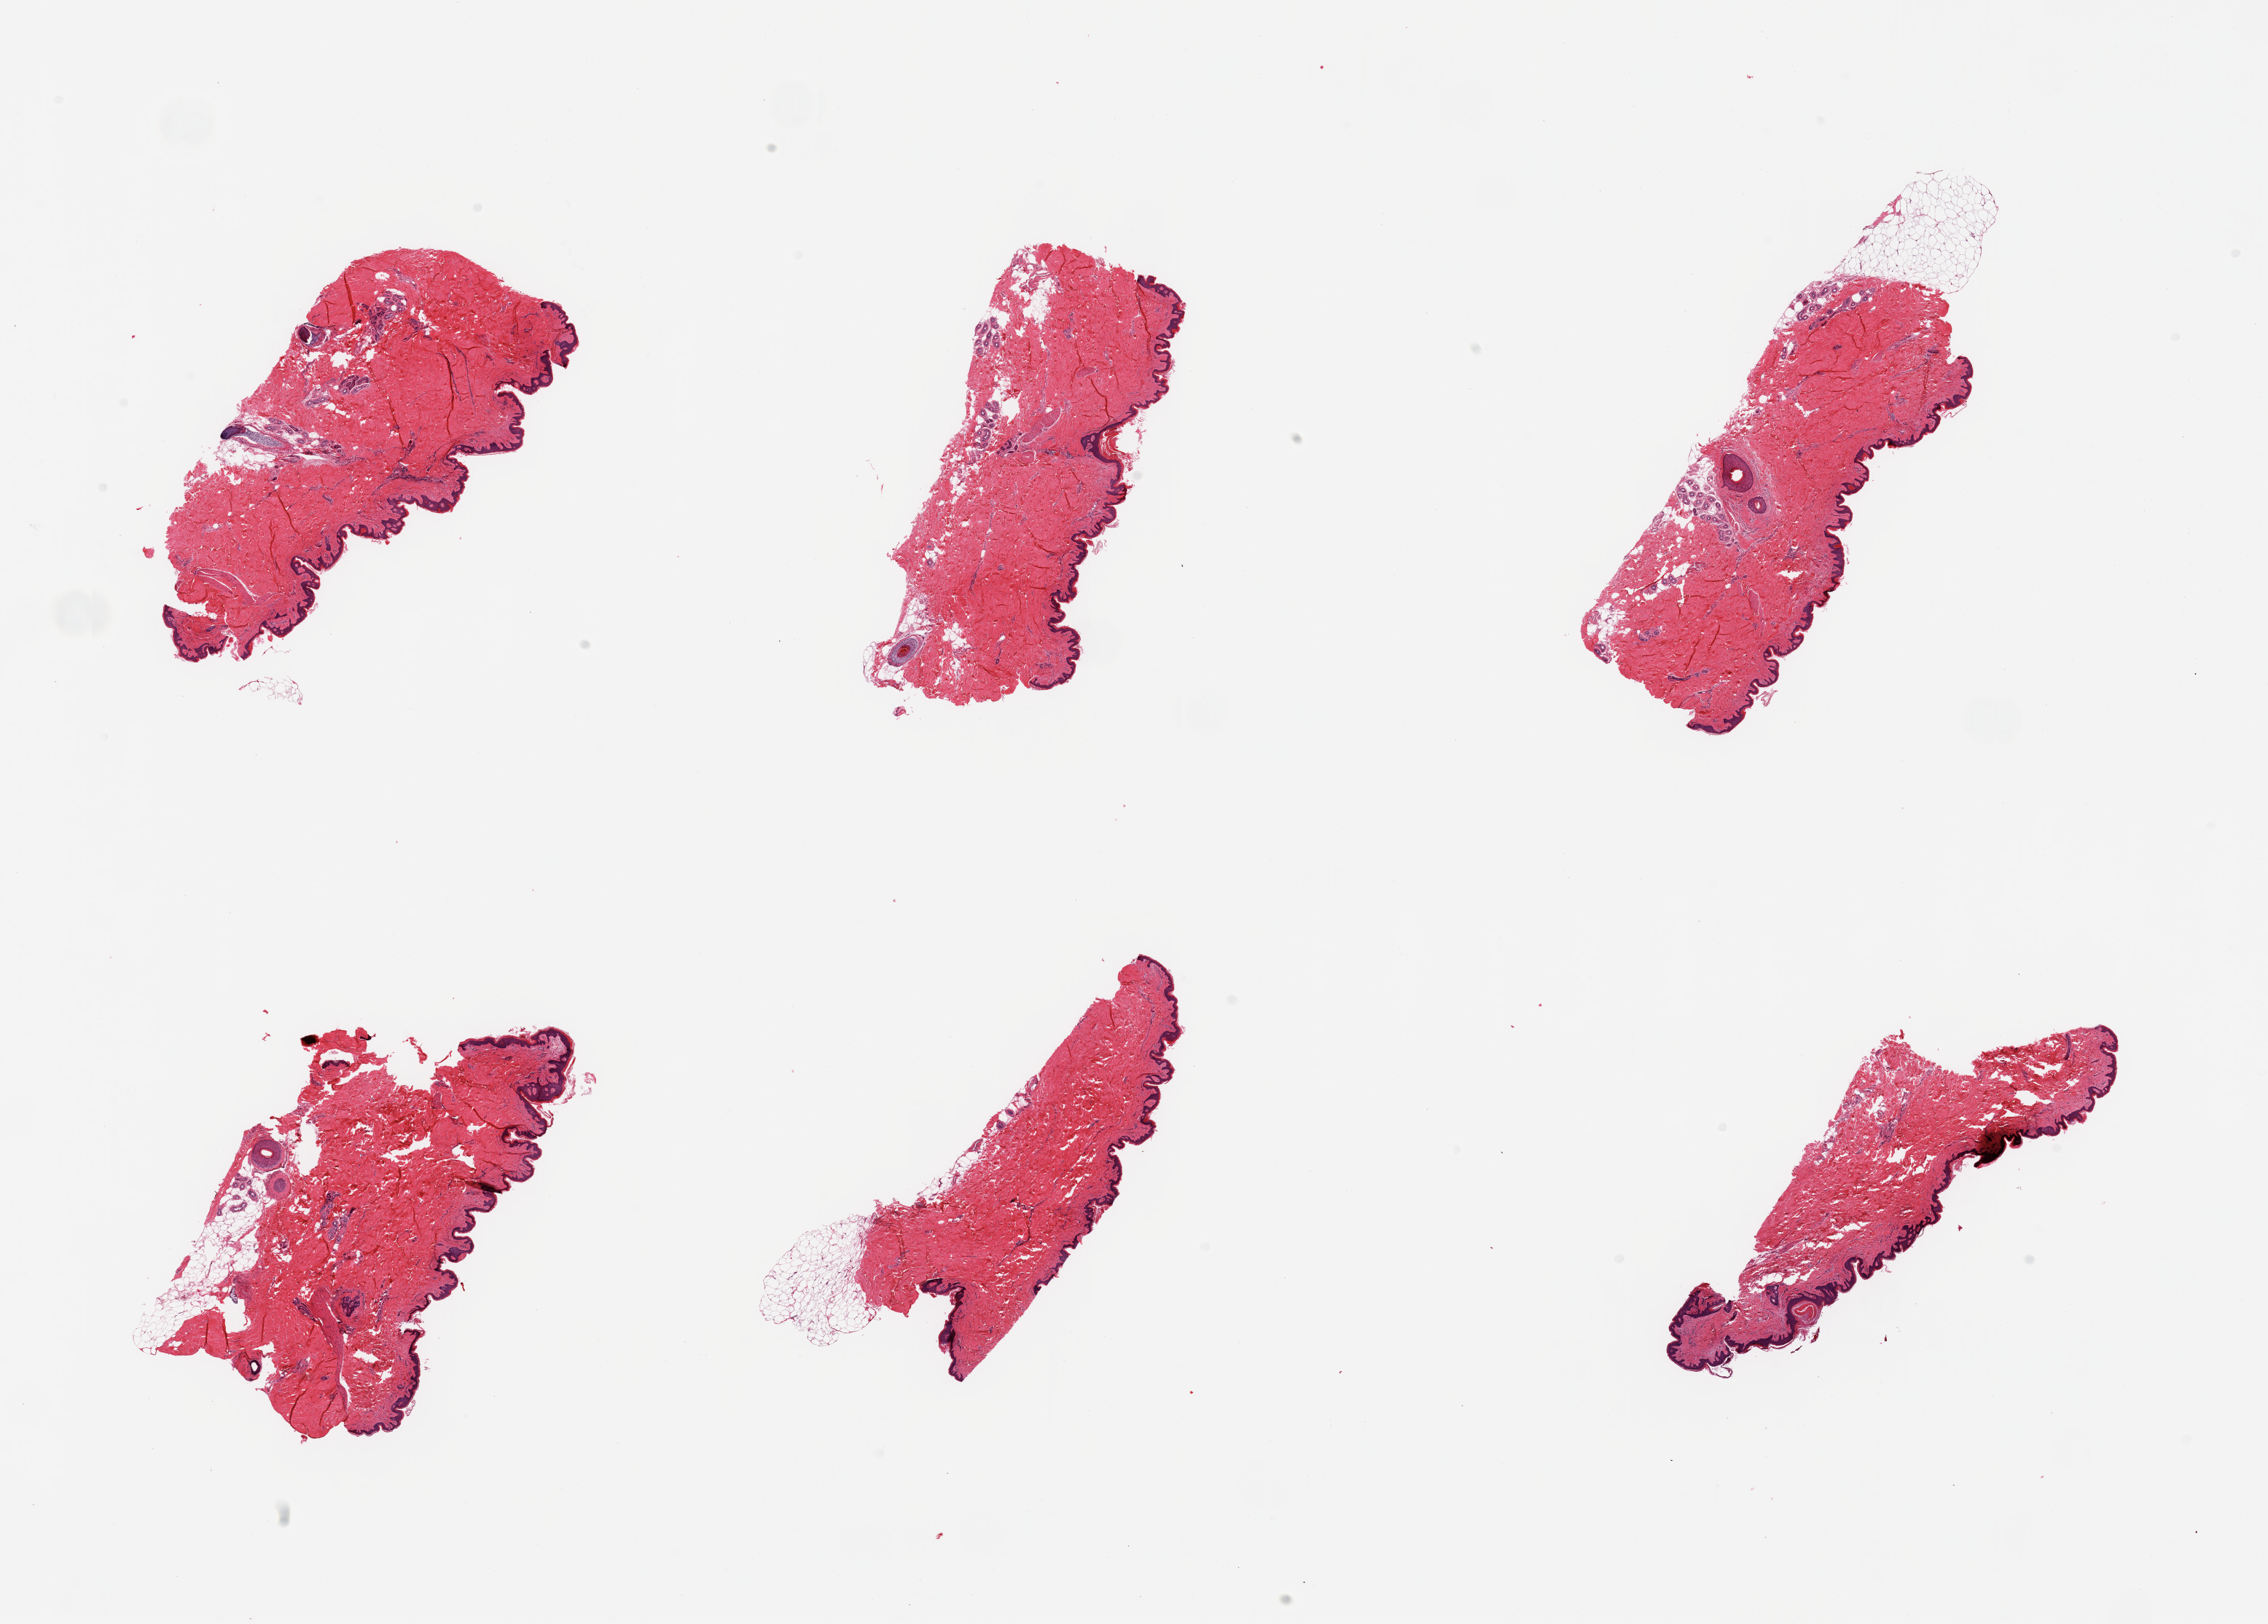
Whole-slide image, hematoxylin and eosin (H&E) stain, brightfield — shown as a low-resolution overview of the whole scanned area (about 24.6 x 17.6 mm, from a 20x scan), PAXgene-fixed, paraffin-embedded tissue, sampled site (target tissue): skin of suprapubic region, donor tissue sample. Donor: male.
Pathologist's review note for this sample: 6 pieces; well trimmed; 10% dermal fat content.